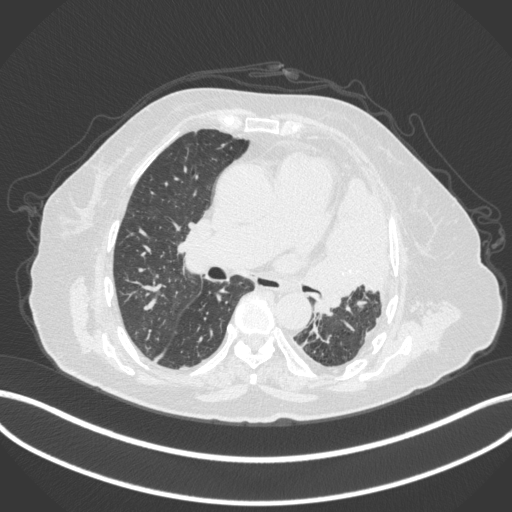
Chest CT, one axial slice. Slice 210 of 399 in the series (ordered by position). Reconstruction kernel B31f. 120 kVp. Lung window (W 1500 / L -600 HU). 1 mm slice thickness. 512 × 512 image matrix, field of view 400 × 400 mm. Patient: female, 75 years. Case-level facts recorded for this patient, not image findings: clinical TNM (as recorded): T3 N3 M1.
Outlined on this slice (rectangle marked by the reading radiologist):
- lung tumour (recorded histology: adenocarcinoma): bounding box <294,171,394,318> (left, top, right, bottom; pixels)